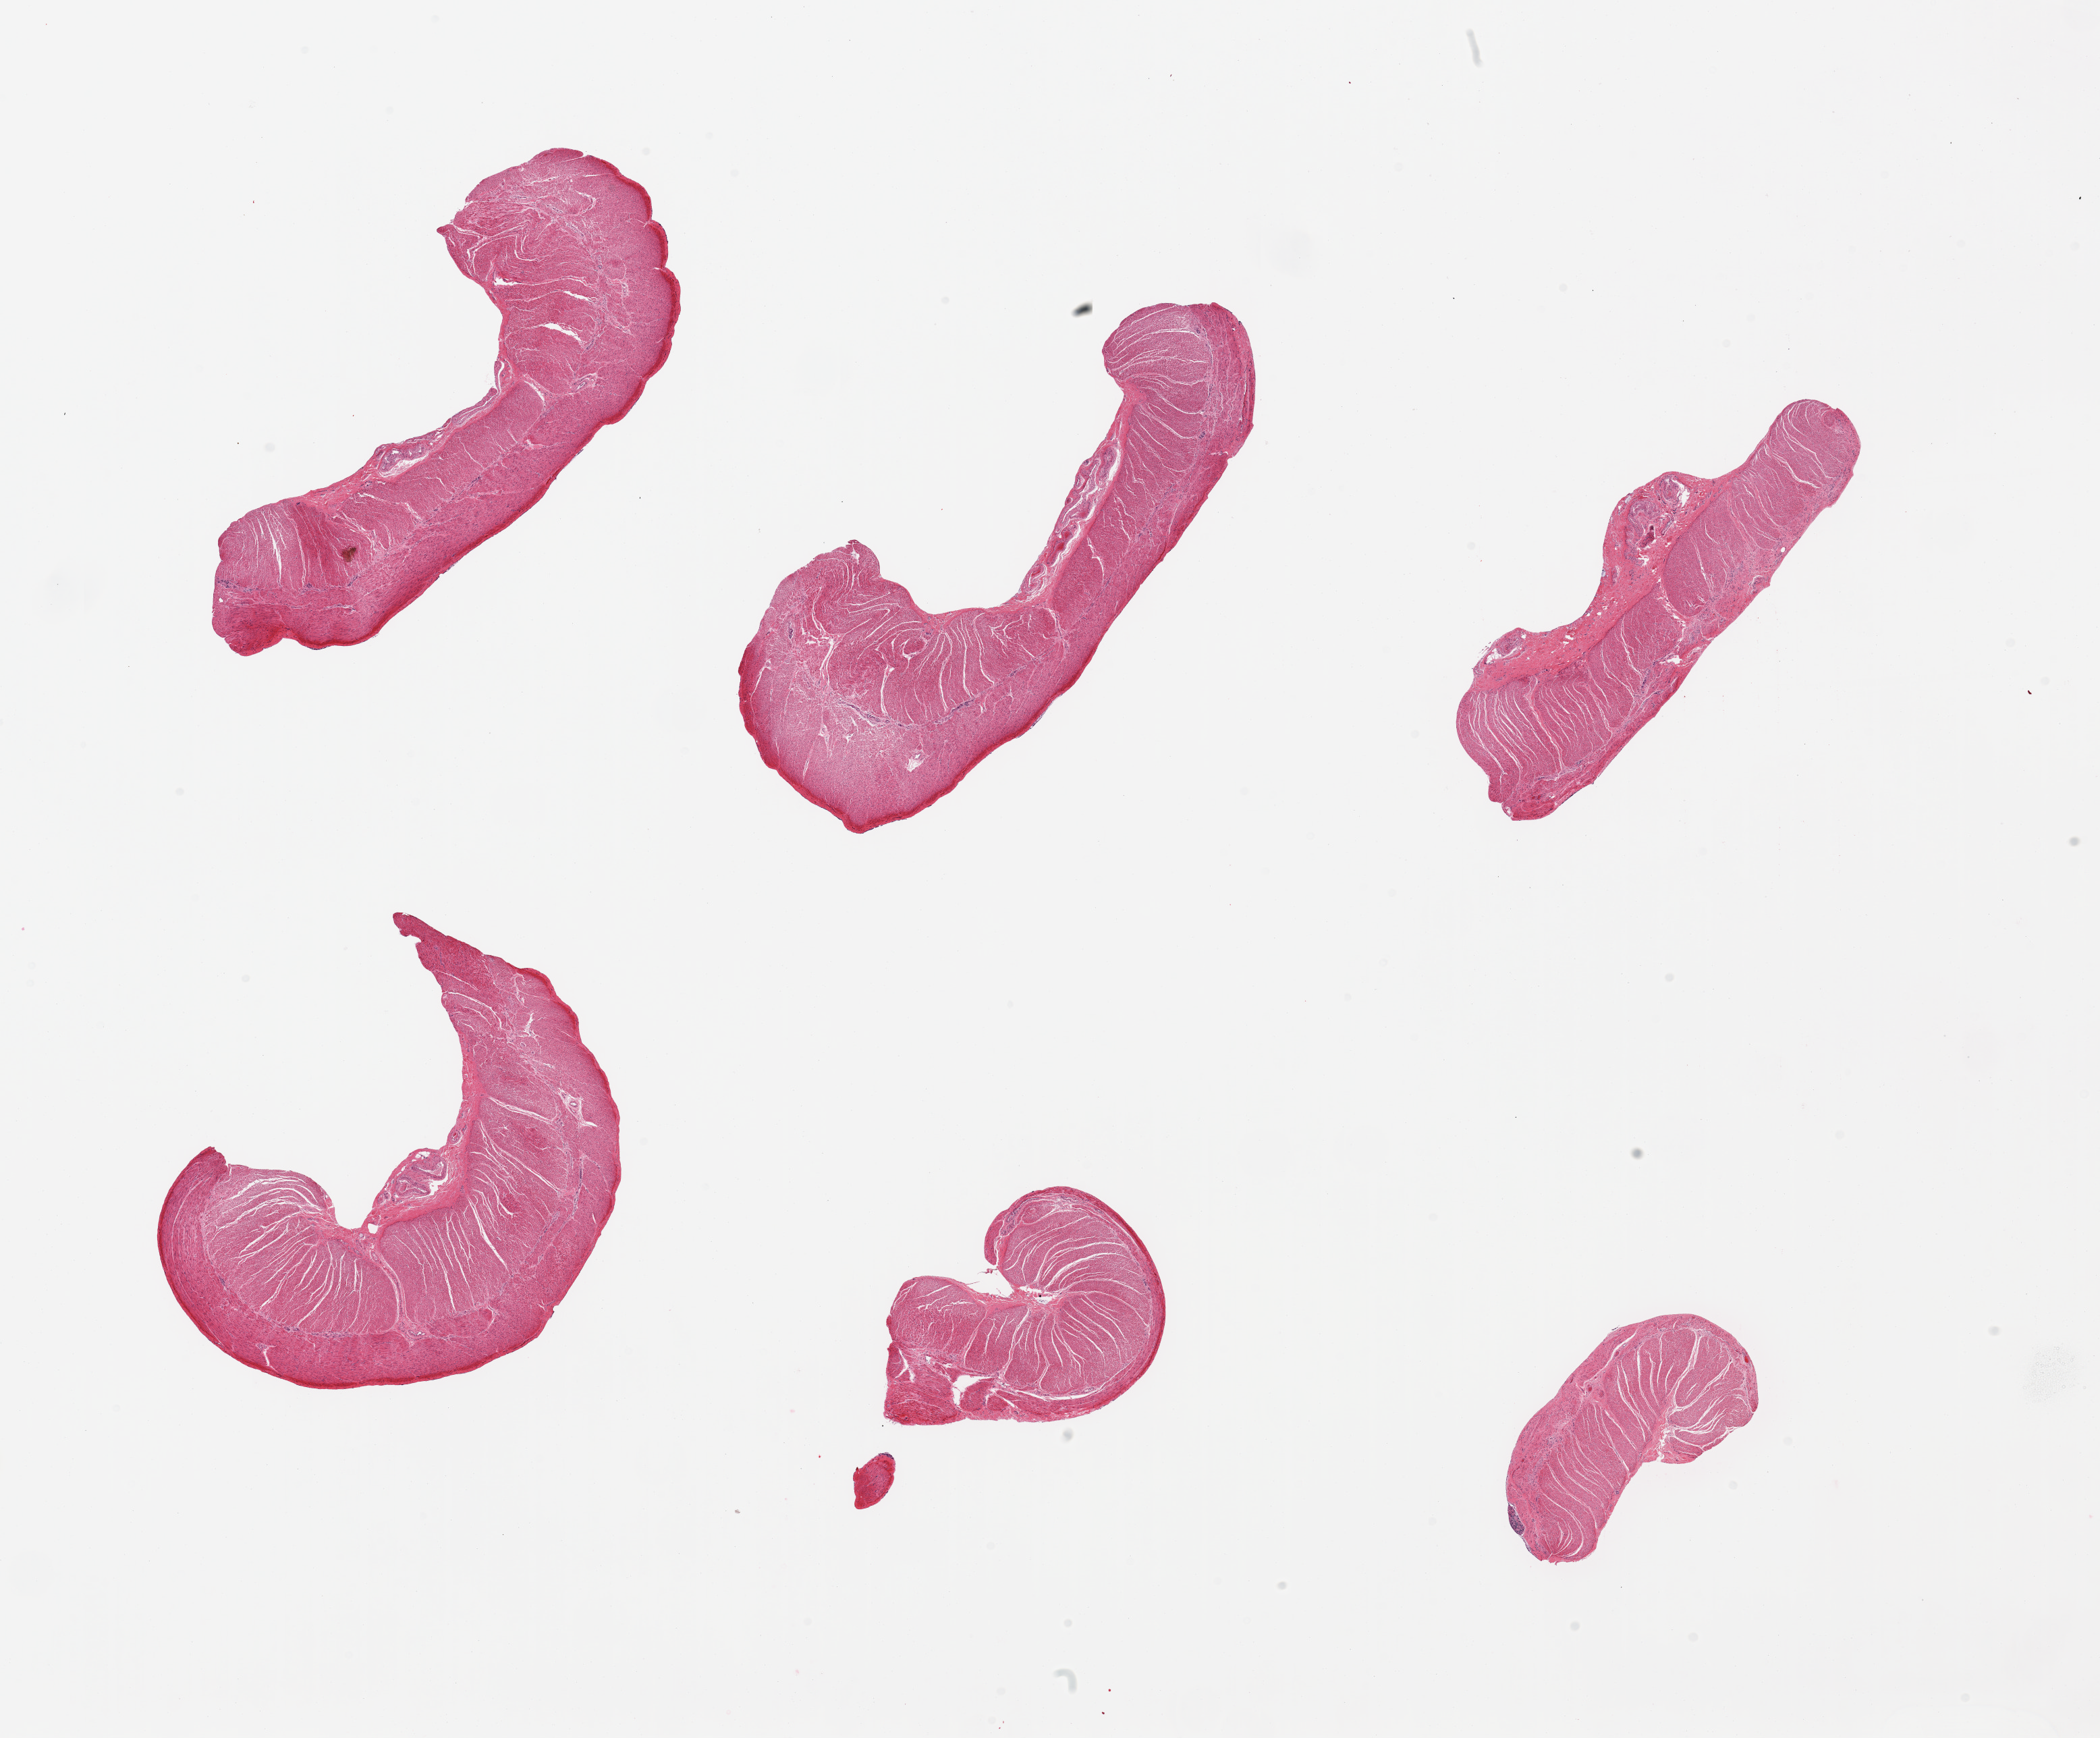
Digitized haematoxylin and eosin-stained section — low-resolution overview of the scanned area, about 24.6 x 20.4 mm (acquisition: 20x scan). PAXgene-fixed paraffin-embedded (PFPE) section. Target tissue: sigmoid colon. Donor tissue sample.
• reviewer comment on this tissue sample: 6 pieces, all target muscularis